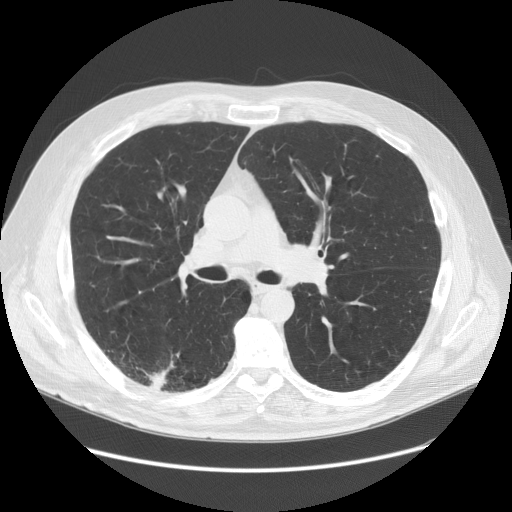
Low-dose screening chest CT, one axial slice; slice 87 of 149 in the series (ordered by position); reconstruction kernel STANDARD; lung window (W 1500 / L -600 HU); 2.5 mm slice thickness; 512 × 512 image matrix.
Annotated regions visible in this slice (expert manual segmentation):
- lesion 1 (tumor, lower lobe of right lung): bounding box [x1, y1, x2, y2] px = [149, 365, 173, 390]